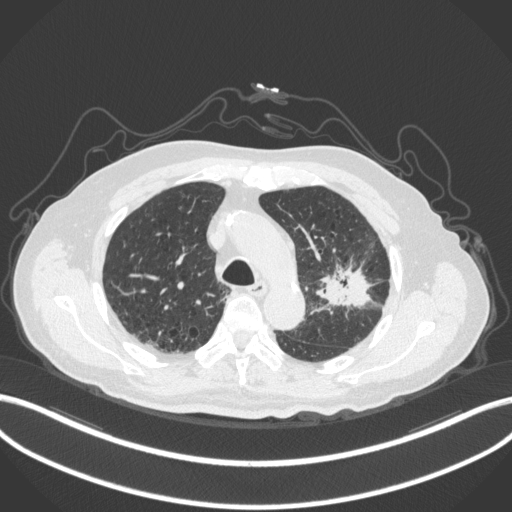
Chest CT, one axial slice; position 213 of 331 along the scan axis; reconstruction kernel B31f; 120 kVp; lung window (W 1500 / L -600 HU); 1 mm slice thickness; 512 × 512 image matrix. Male patient, age 79 years. Case-level facts recorded for this patient, not image findings: clinical TNM (as recorded): T2a N1 M1.
Structures marked on this image (bounding box drawn by a radiologist):
- lung tumour (recorded histology: adenocarcinoma): bounding box (x1, y1, x2, y2) in pixels: (312, 252, 379, 314)